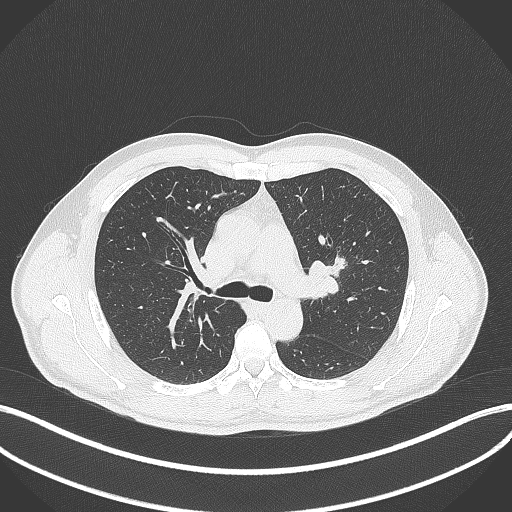
Chest CT, one axial slice; position 275 of 392 along the scan axis; reconstruction kernel B70f; 120 kVp; lung window (W 1500 / L -600 HU); 1 mm slice thickness; 512 × 512 image matrix, field of view 400 × 400 mm. Patient: male, 50 years. From the clinical record (not read from this slice): clinical TNM (as recorded): T1c N1 M1b.
Structures marked on this image (rectangle marked by the reading radiologist):
- lung tumour (recorded histology: squamous cell carcinoma): bounding box [x1, y1, x2, y2] px = [322, 250, 349, 277]